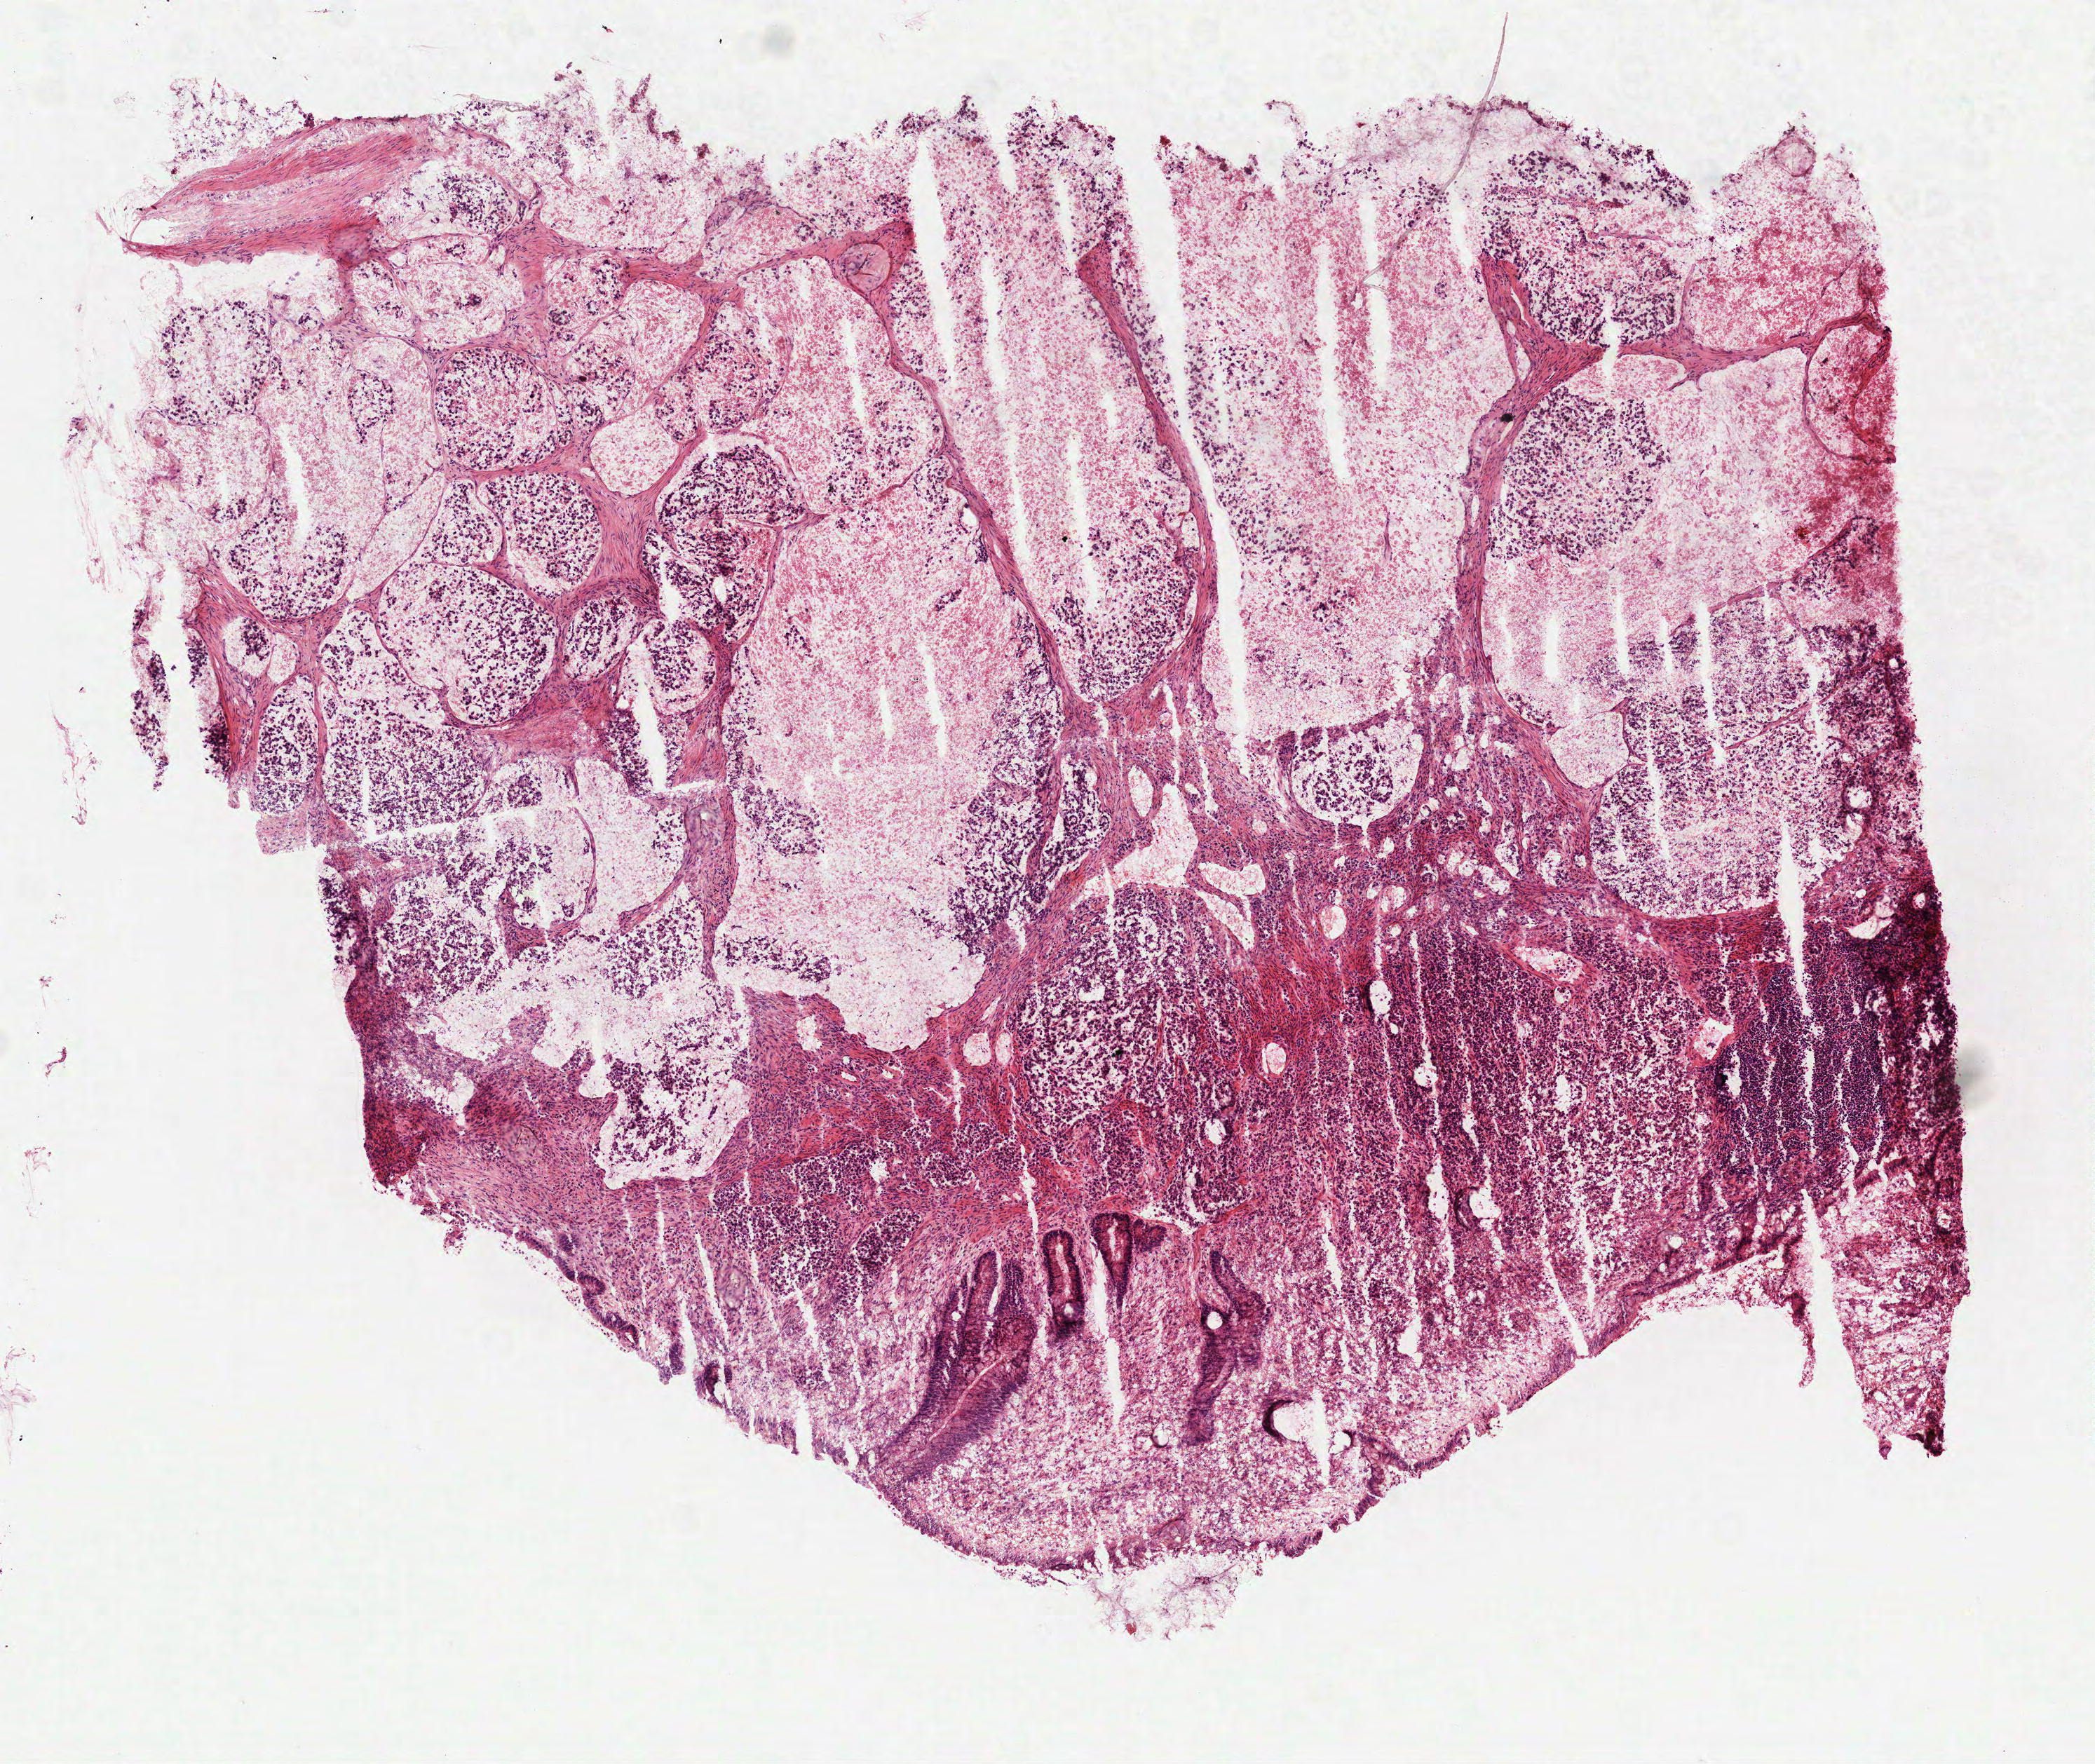
H&E whole-slide image, whole scanned area (about 6.0 x 5.1 mm) shown as a low-resolution overview, frozen section, rectum, primary tumour sample. Patient: female, age at initial diagnosis 37 years. Pathologist review of this section (percent, as recorded): tumour cells 85%, tumour nuclei 75%, normal cells 5%, stromal cells 10%, necrosis 0%.
- lymph nodes positive (case pathology): 30 of 30 examined
- histologic diagnosis: Mucinous adenocarcinoma (rectosigmoid junction)